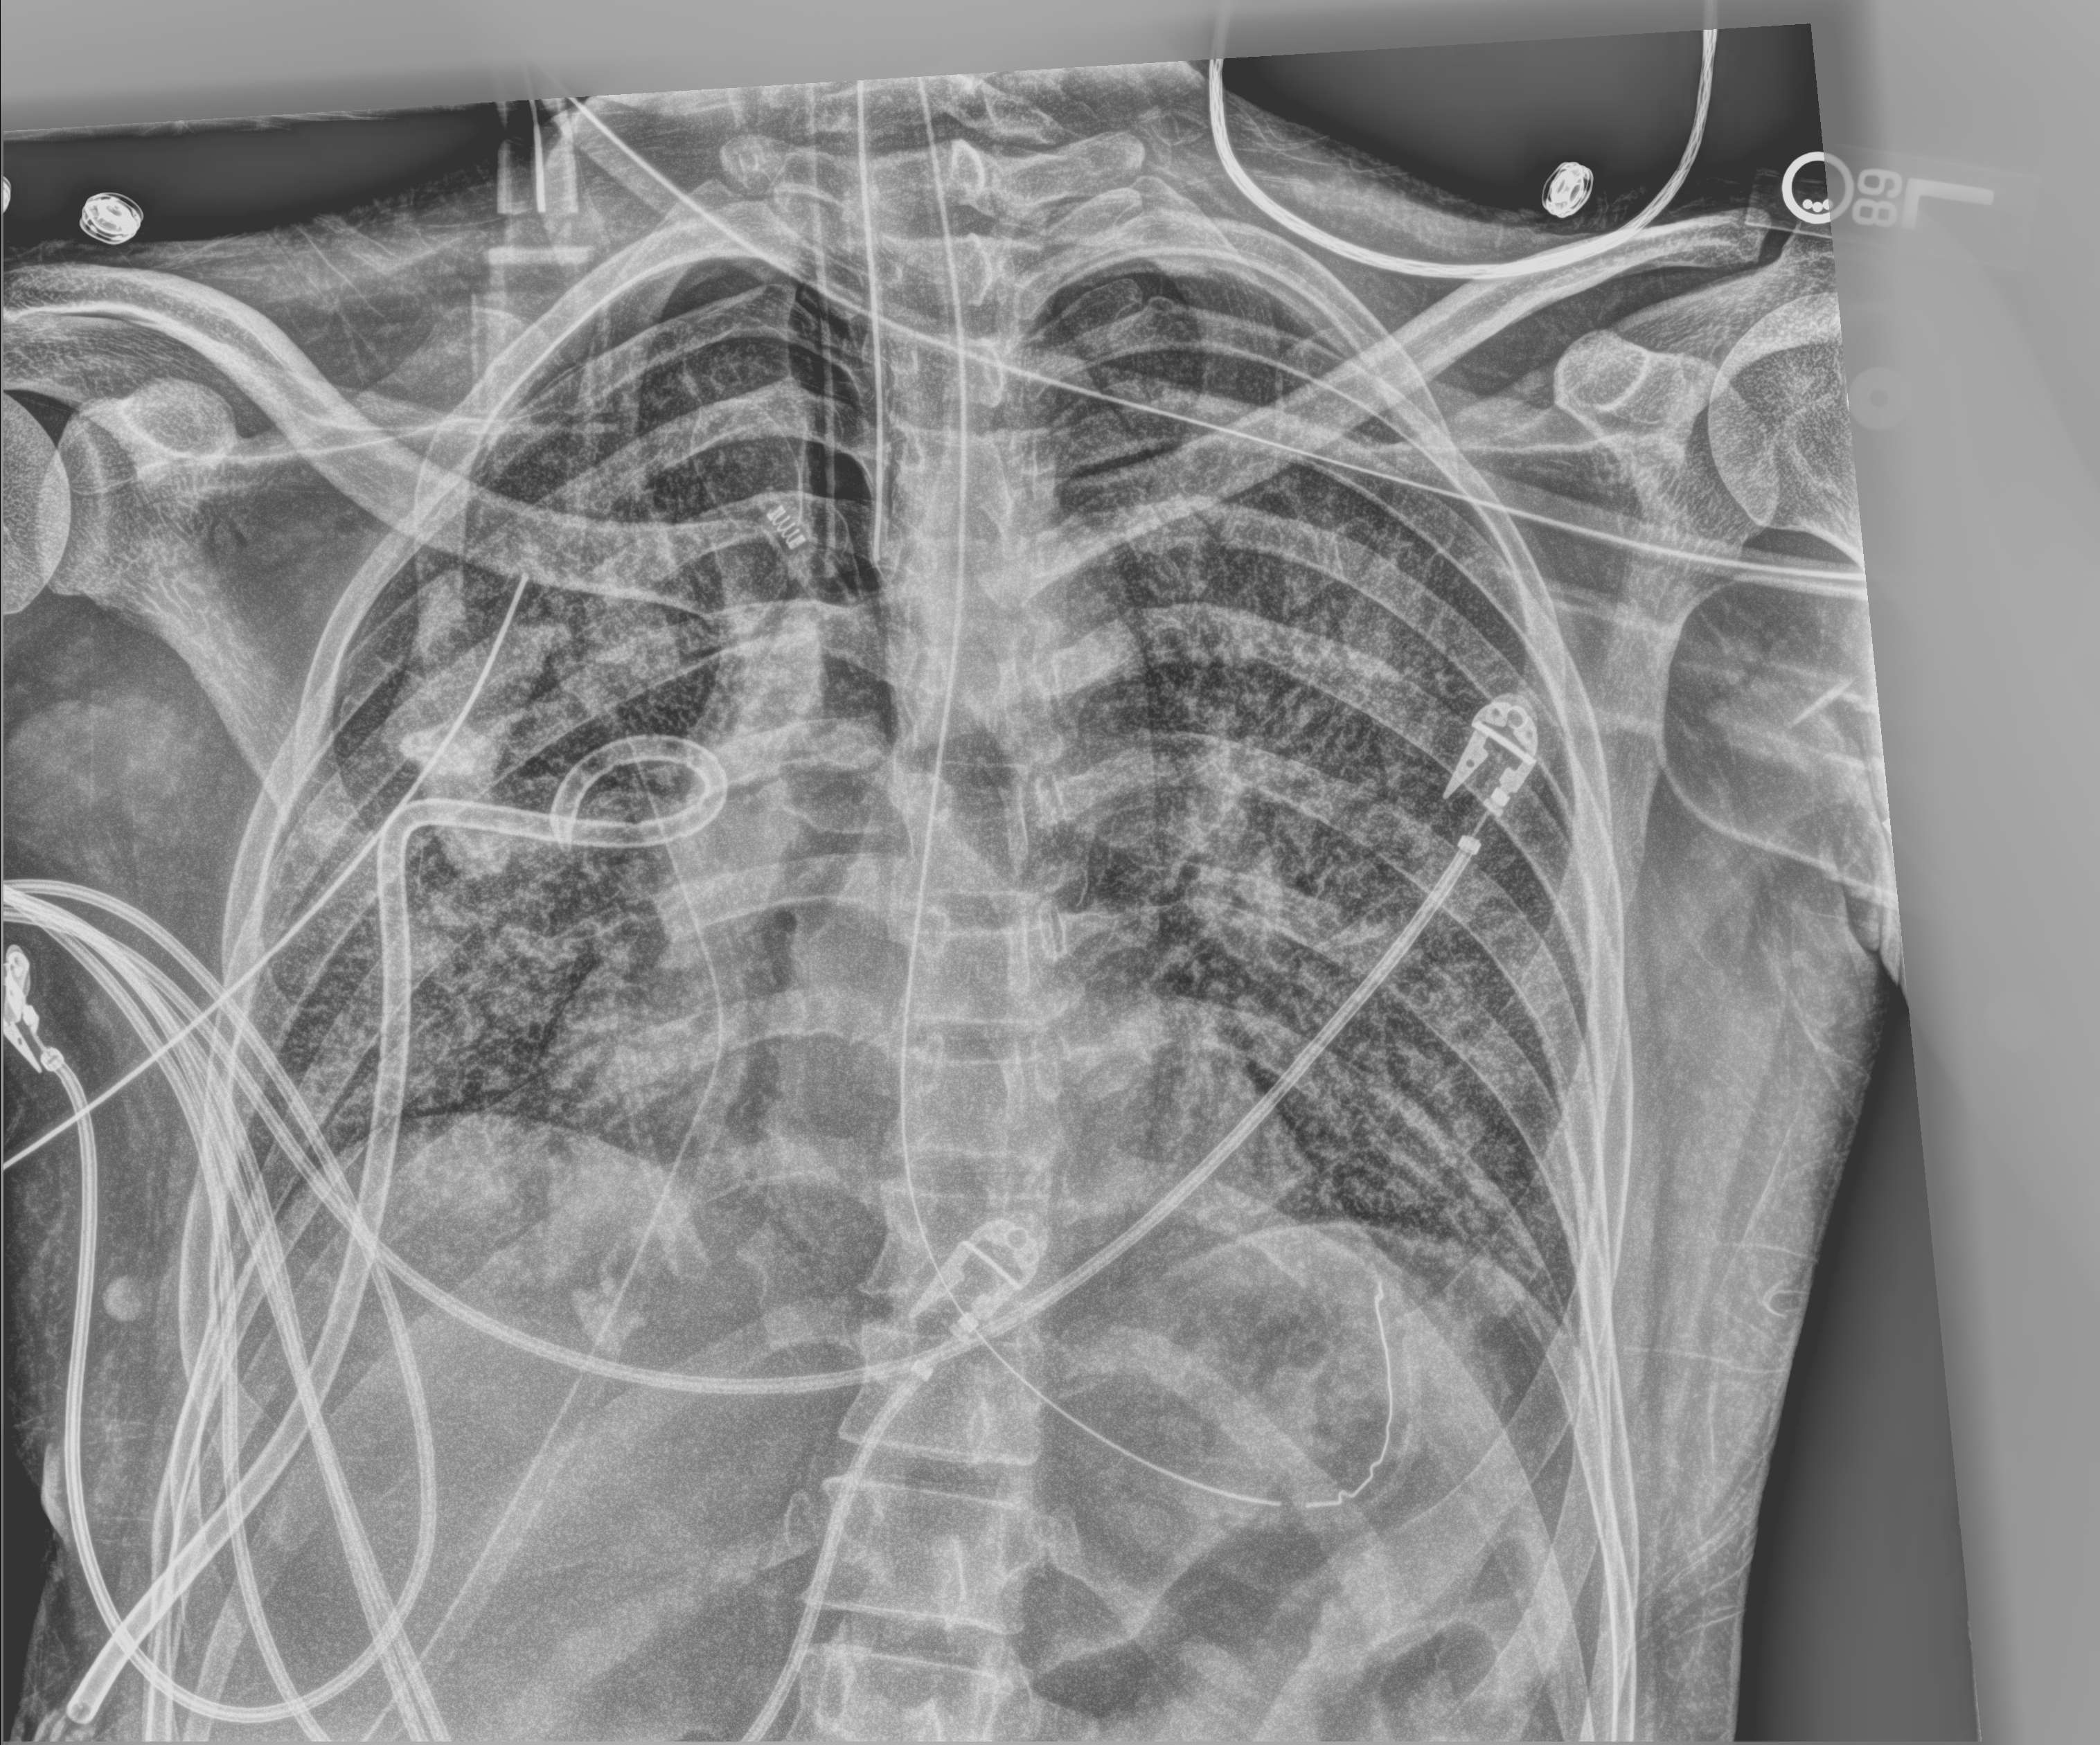
Chest X-ray (portable). Adult patient hospitalised with COVID-19, age 18–59 years.
From the hospital-stay record, not from the radiograph (when in the stay this image was taken is not recorded): admitted to intensive care during this hospital stay: yes; diabetes (admission record): no; length of hospital stay: 41 days.